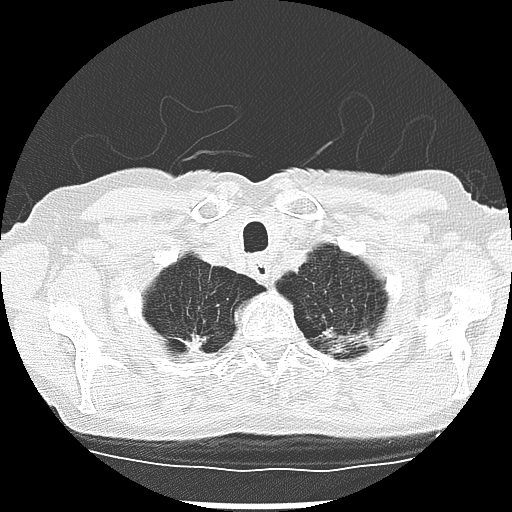
Low-dose screening chest CT, one axial slice; position 246 of 265 along the scan axis; reconstruction kernel LUNG; 120 kVp; lung window (W 1500 / L -600 HU); 2.5 mm slice thickness; 512 × 512 image matrix, field of view 300 × 300 mm.
Structures marked on this image (manually delineated by an expert):
- lesion 2 (tumor, upper lobe of right lung): box from (x=185, y=334) to (x=205, y=351) px